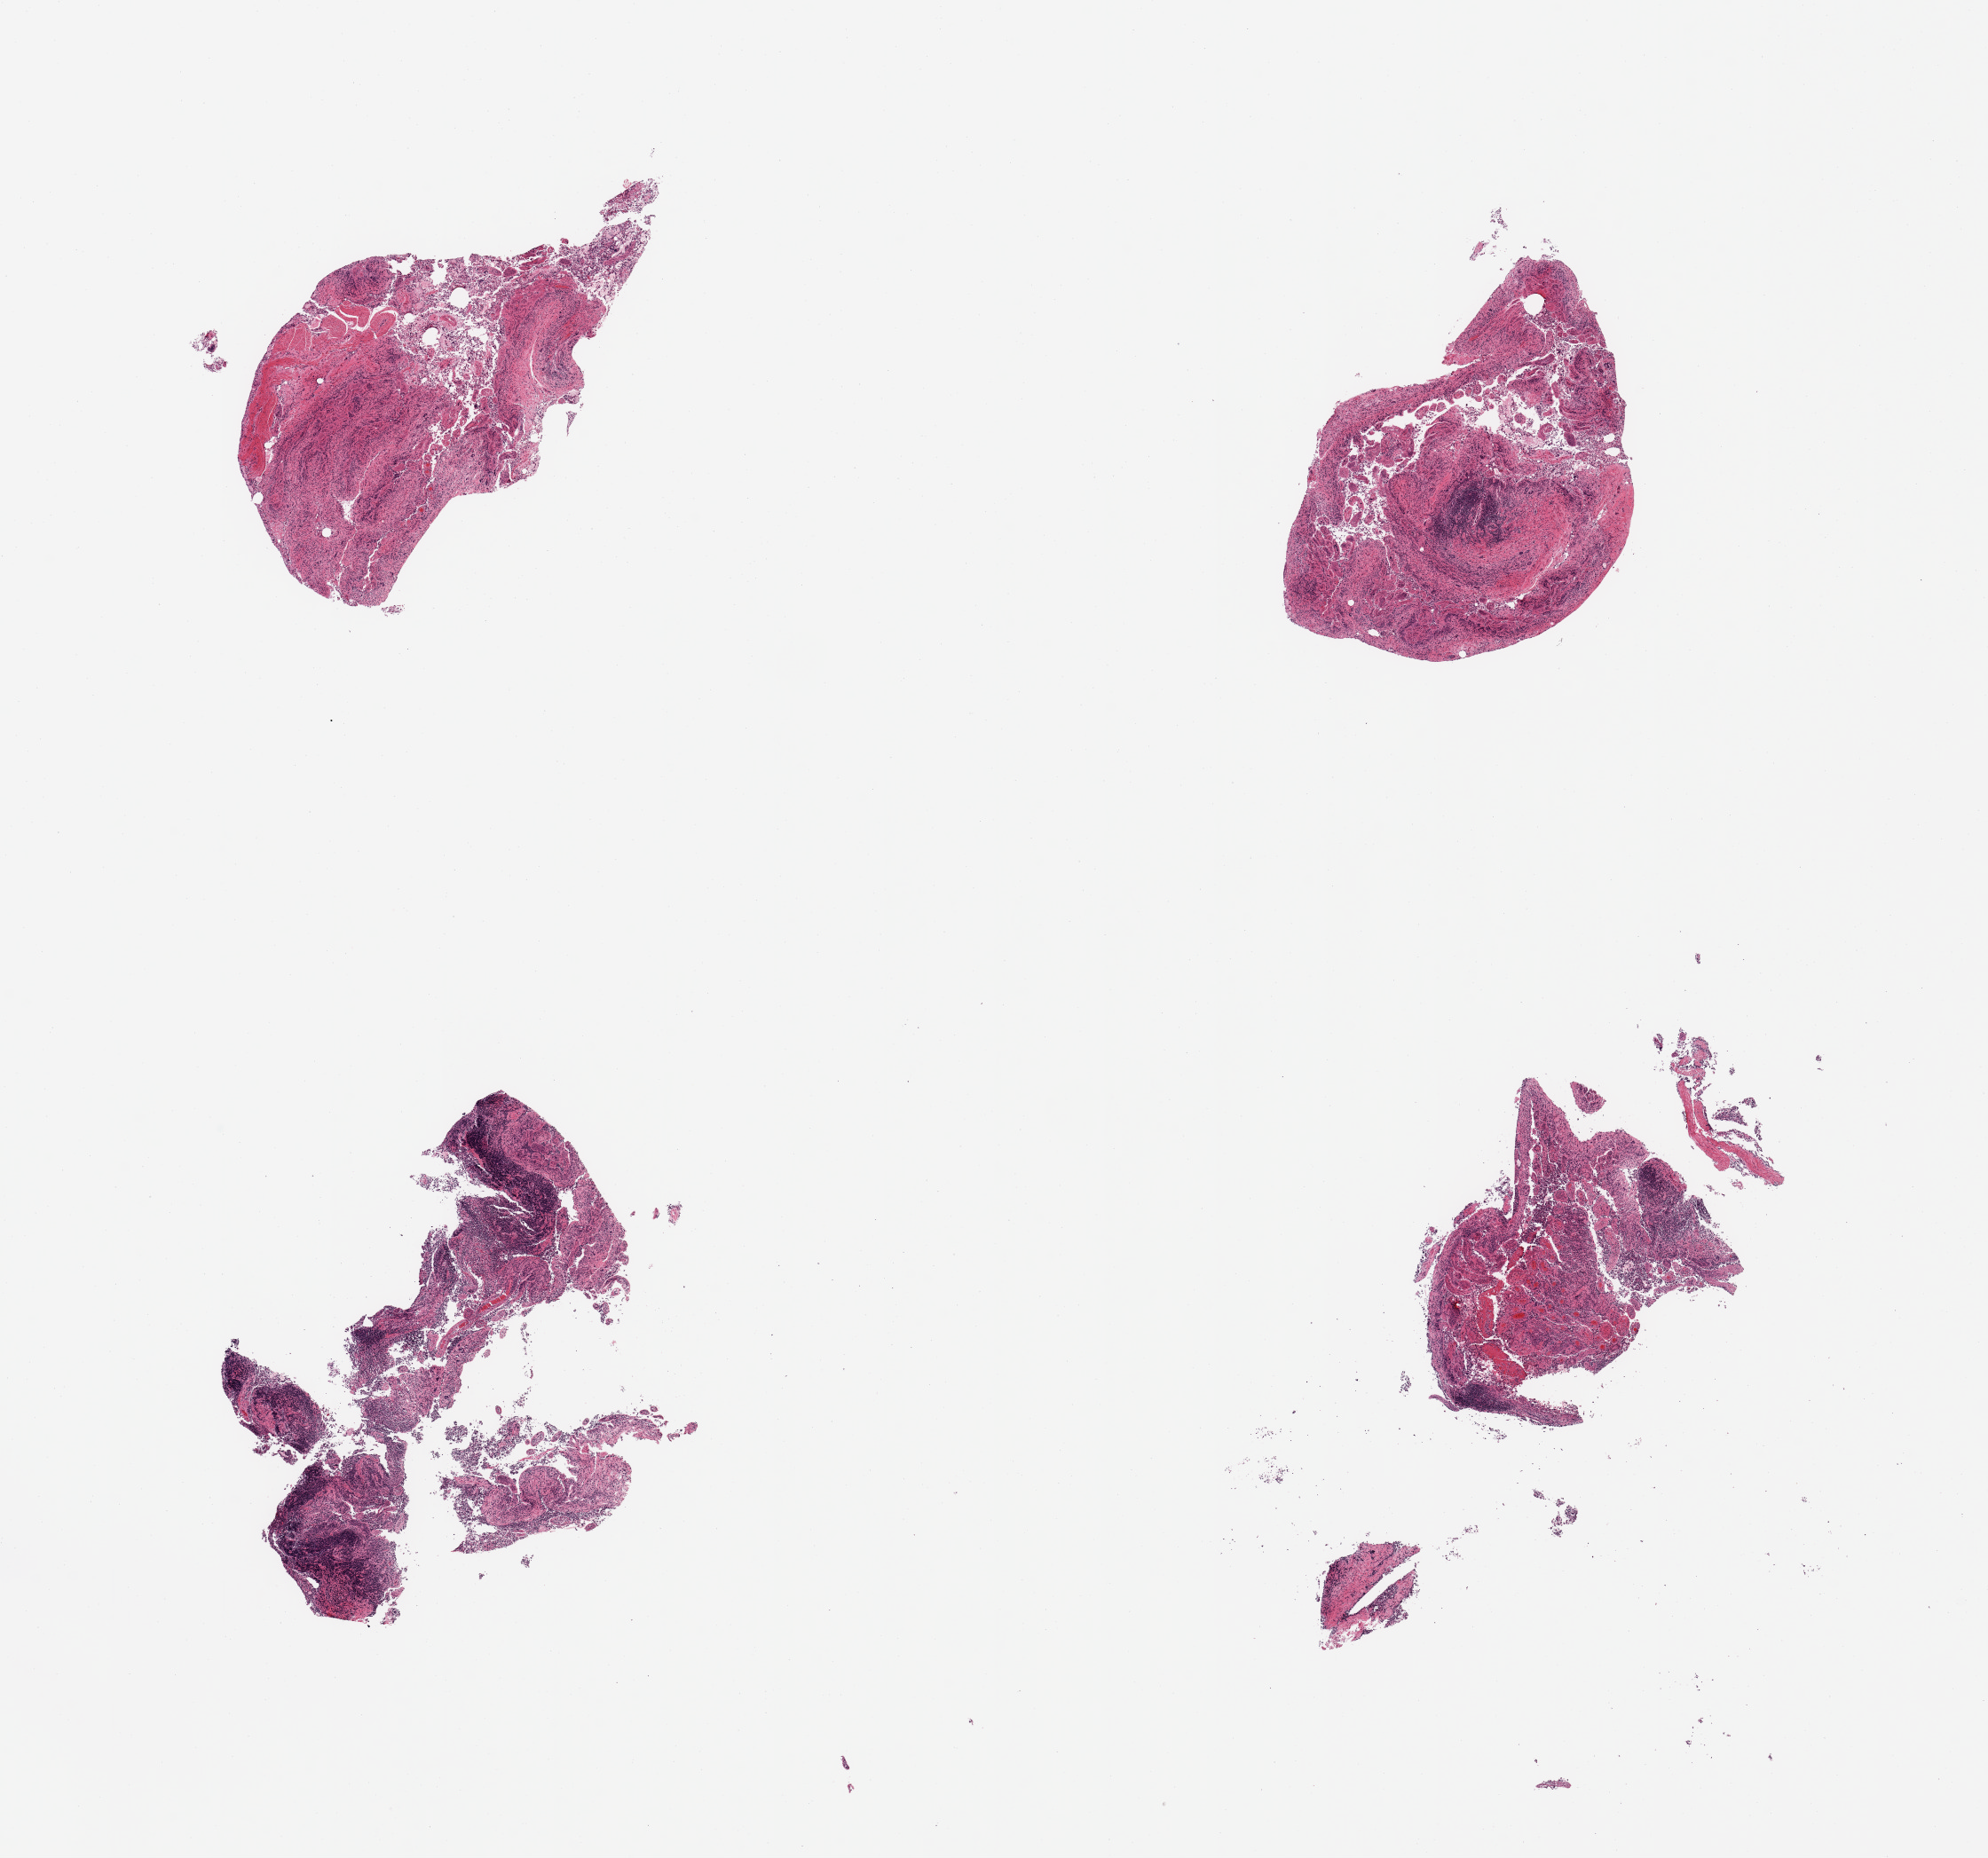
Digitized haematoxylin and eosin-stained section, brightfield — a low-resolution overview of the entire scanned area, about 17.7 x 16.6 mm, PAXgene-fixed paraffin-embedded (PFPE) section, section of ileum (target tissue), tissue donor sample. Donor: female.
- pathologist's review note for this sample: 4 pieces, glandular mucosa totallly autolyzed; target lymphoid aggregates are ~20% of residual tissue